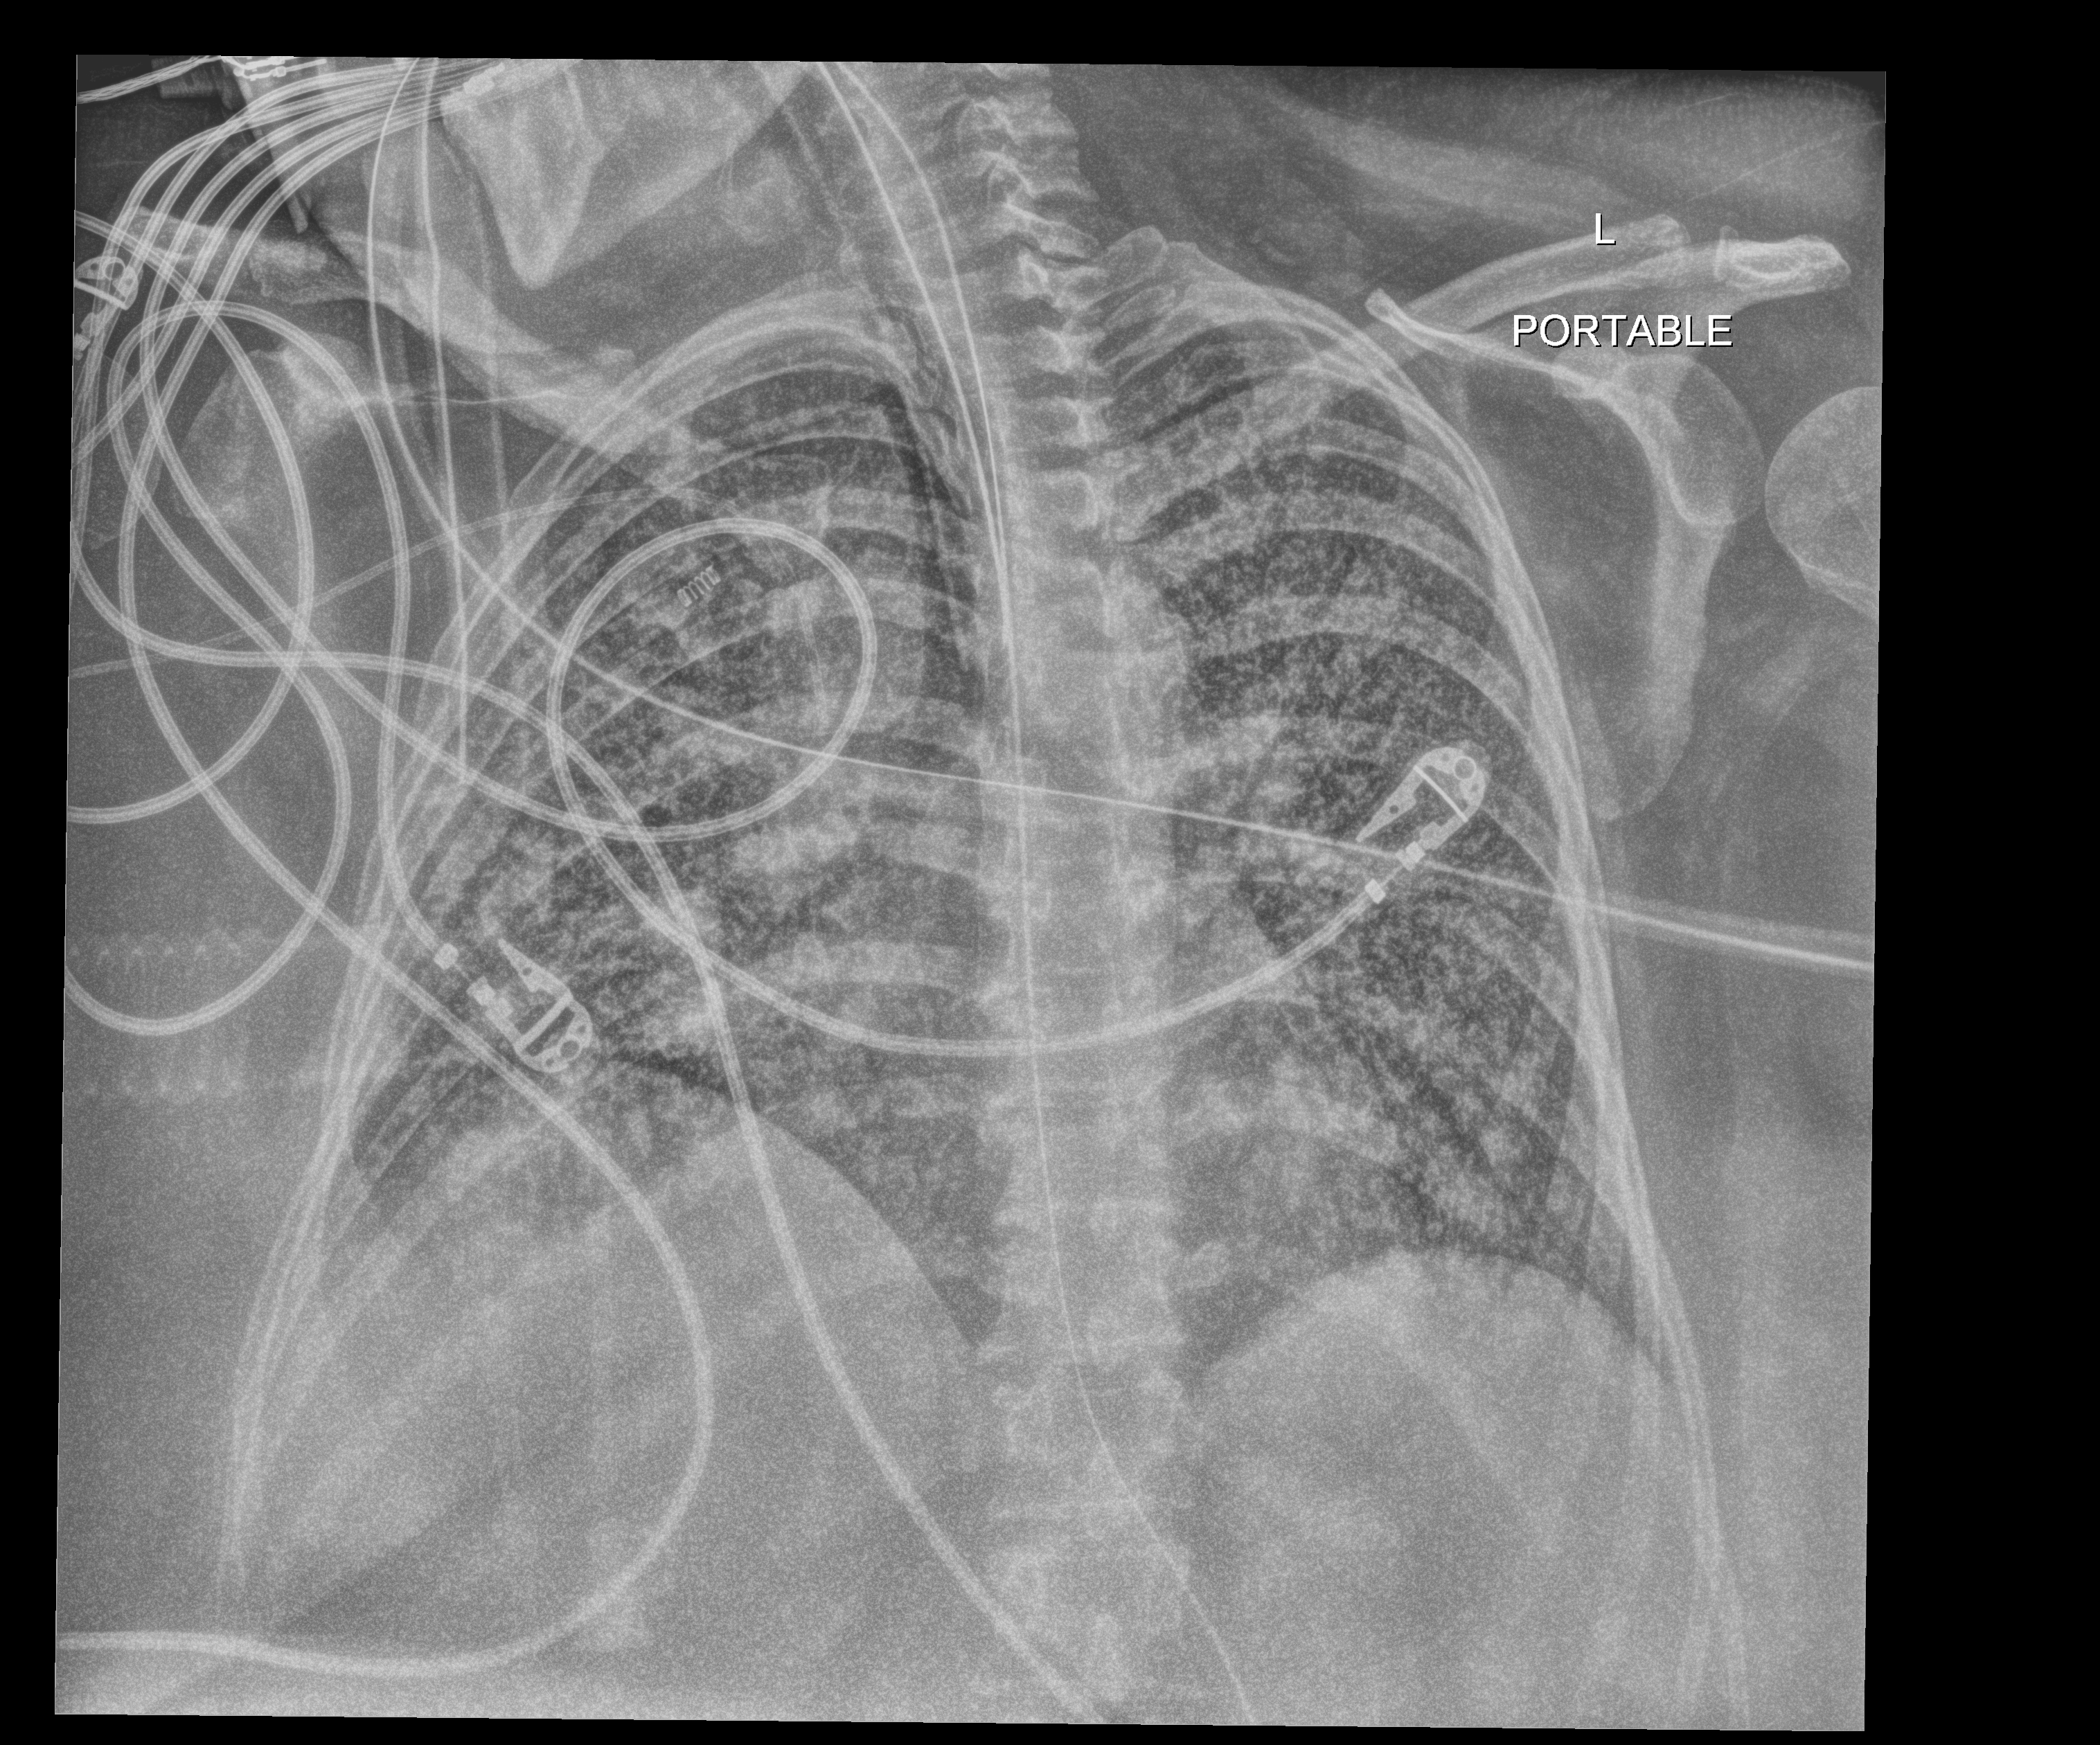
Portable chest radiograph; anteroposterior (AP) projection. Female patient hospitalised with COVID-19, age 18–59 years.
From the hospital-stay record, not from the radiograph (when in the stay this image was taken is not recorded):
- admitted to intensive care during this hospital stay: yes